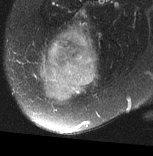
MRI of an extremity soft-tissue mass, one axial slice. Slice 24 of 77 in the series (ordered by position). T2-weighted fat-saturated. MR volume resampled by the dataset authors to the PET/CT grid (not the native acquisition matrix). 153 × 156 image matrix. Female patient. From the clinical record (not read from this slice): histological type: synovial sarcoma; grade: intermediate; site of the primary tumour: right buttock.
Annotated regions visible in this slice (expert contour drawn on MRI and transferred to this co-registered scan by the dataset authors):
- gross tumour volume including surrounding oedema: bounding box [x1, y1, x2, y2] px = [35, 22, 98, 101]
- gross tumour volume (mass): [39, 29, 97, 101]